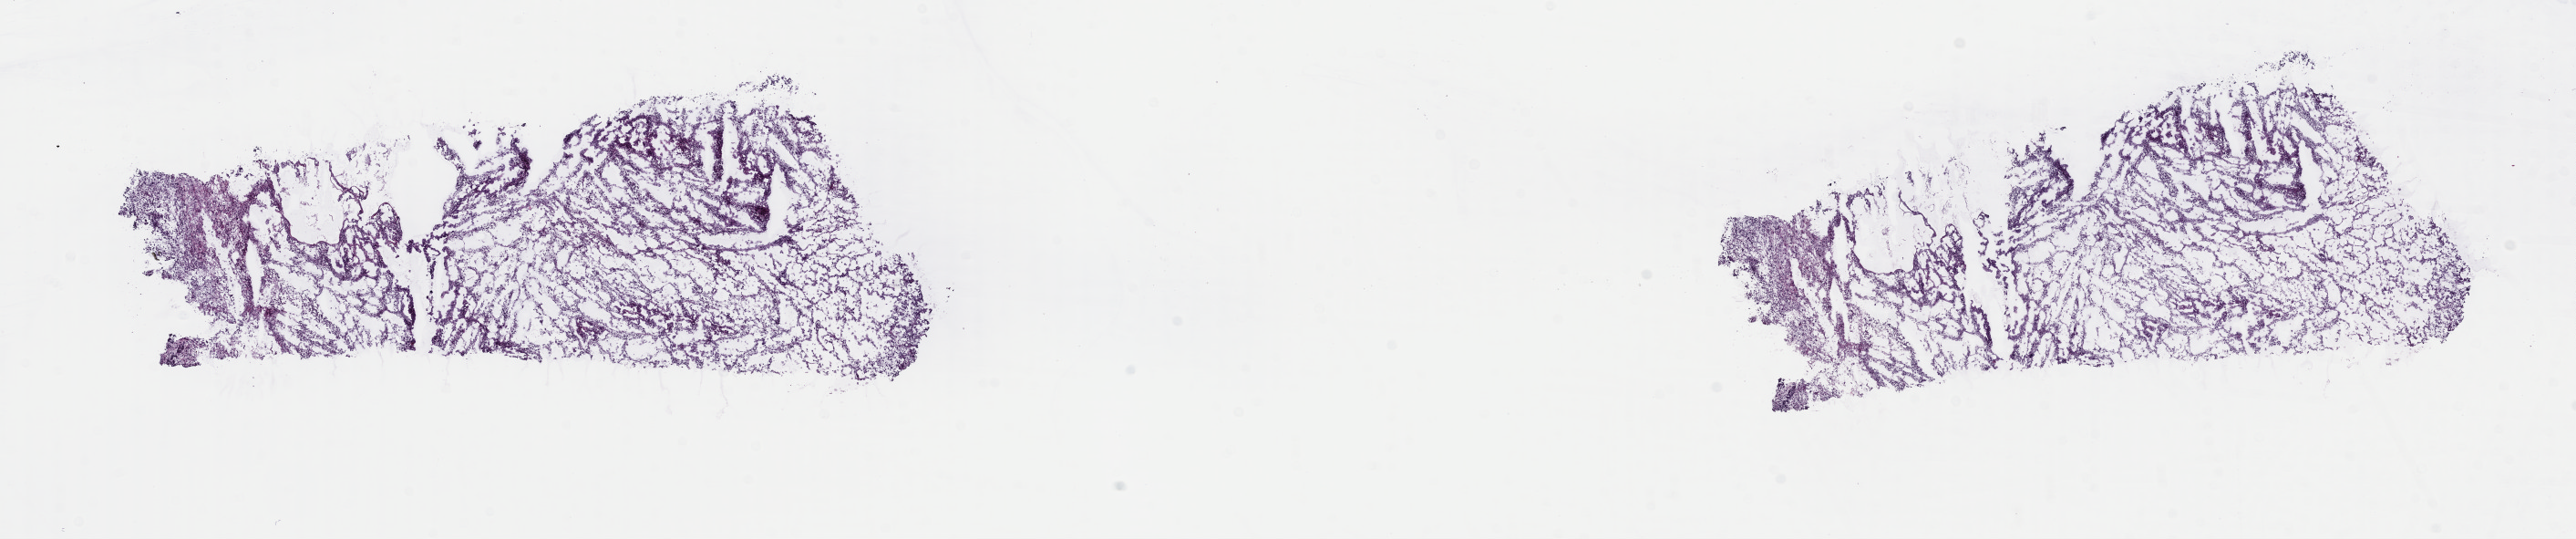
Digitized Hematoxylin and eosin (H&E) stained tissue section (whole slide) — low-resolution overview of the scanned area, about 22.3 x 4.7 mm (from a 40x scan). Frozen section. Sample: primary tumour, uterus. Female patient; age at initial diagnosis 54 years. Slide review estimates, as recorded: tumour cells 70%, tumour nuclei 70%, normal cells 0%, stromal cells 20%, necrosis 10%. Inflammatory infiltration, as recorded: lymphocyte infiltration 40%, monocyte infiltration 20%, neutrophil infiltration 20%.
Diagnosis: Mullerian mixed tumor. Lymph nodes positive (case pathology): 0 of 1 examined. FIGO stage: IIIC2.